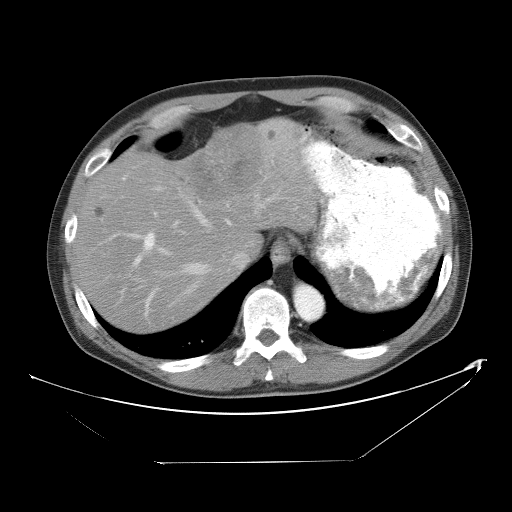
Contrast-enhanced abdominal CT, one axial slice; slice 42 of 53 in the series (ordered by position); 120 kVp; intravenous contrast given; soft-tissue window (W 400 / L 40 HU); 5 mm slice thickness; 512 × 512 image matrix. Male patient, age 59 years. Case-level facts recorded for this patient, not image findings: diagnosis: colorectal cancer liver metastases, imaged before liver resection; multiple liver metastases: yes; largest metastasis: 8.5 cm; disease in both lobes: no.
Structures marked on this image (outlined manually by an expert reader):
- hepatic veins: bounding box [x1, y1, x2, y2] px = [154, 186, 275, 307]
- liver: [76, 125, 317, 330]
- planned liver remnant (the part of the liver to remain after resection): [76, 161, 232, 330]
- portal vein (with intrahepatic branches): [110, 205, 264, 312]
- liver metastasis: [96, 205, 106, 218]
- liver metastasis: [269, 132, 277, 142]
- liver metastasis: [191, 127, 263, 203]